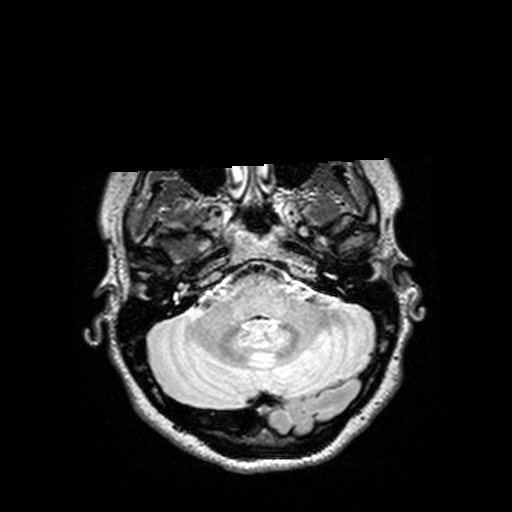
Brain MRI from a brain-tumour surgery series, one axial slice. Position 112 of 144 along the scan axis. T2 FLAIR. 1 mm slice thickness. 512 × 512 image matrix, field of view 250 × 250 mm. Case-level facts recorded for this patient, not image findings: histopathology: Astrocytoma; WHO grade: 3; IDH mutation: yes; tumour location: Right Insular Temporal.
Structures marked on this image (expert manual segmentation):
- tumour: box from (x=157, y=229) to (x=203, y=259) px